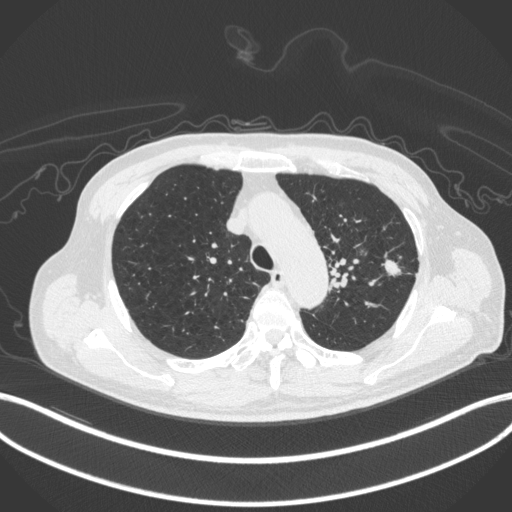
Chest CT, one axial slice. Slice 333 of 420 in the series (ordered by position). 120 kVp. Lung window (W 1500 / L -600 HU). 1 mm slice thickness. 512 × 512 image matrix, field of view 400 × 400 mm. Patient: male, 77 years. From the clinical record (not read from this slice): clinical TNM (as recorded): T3 N1 M0.
Structures marked on this image (bounding box drawn by a radiologist):
- lung tumour (recorded histology: adenocarcinoma): bounding box (x1, y1, x2, y2) in pixels: (380, 253, 402, 278)